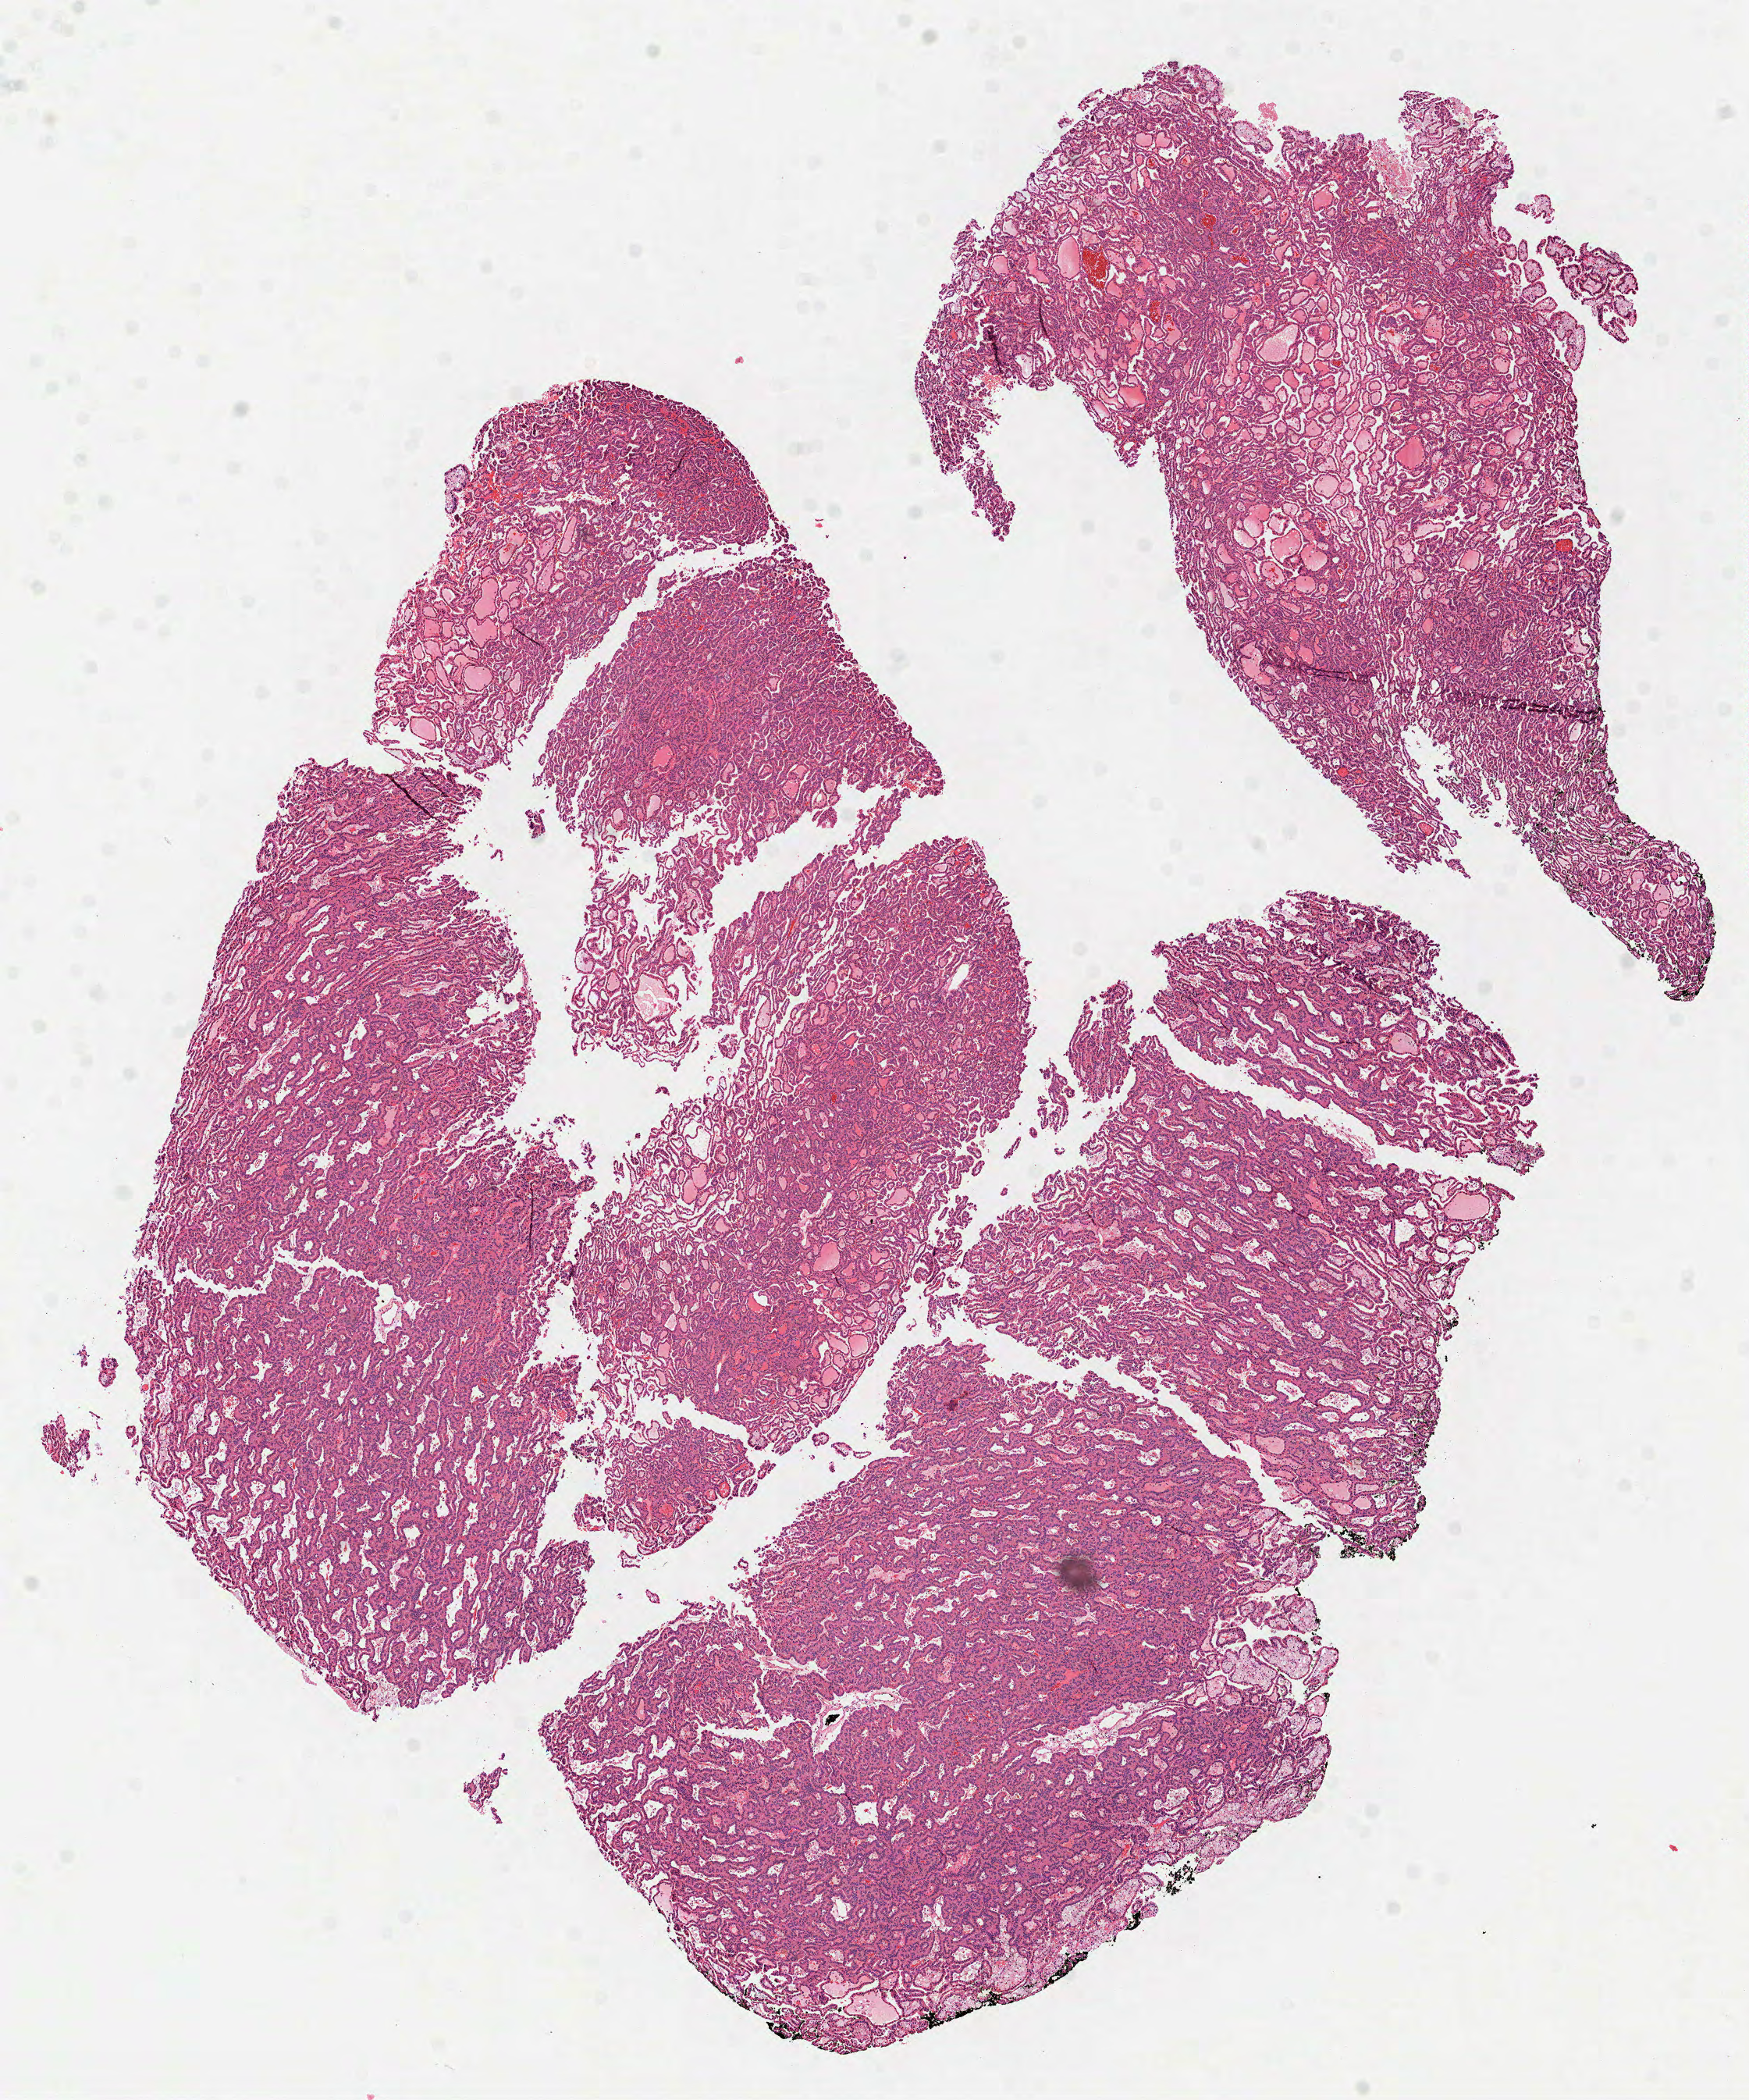
H&E-stained whole-slide image, shown as a low-resolution overview of the whole scanned area (about 9.0 x 10.8 mm), formalin-fixed paraffin-embedded (FFPE) diagnostic section, sample: primary tumour, kidney. Patient: male, age at initial diagnosis 62 years.
• AJCC pathologic stage: III (7th edition)
• diagnosis: Papillary adenocarcinoma, NOS
• laterality: right